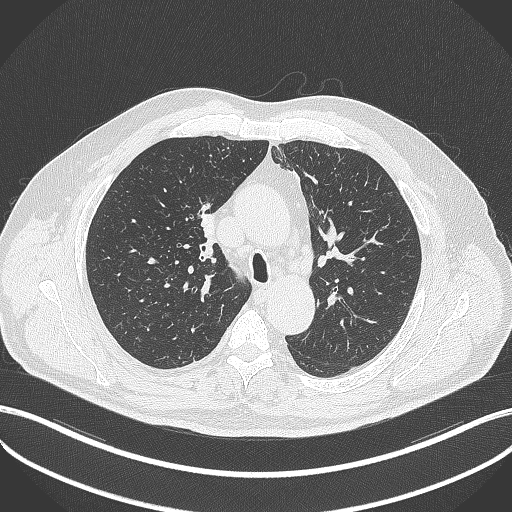
Chest CT, one axial slice. Slice 263 of 411 in the series (ordered by position). Reconstruction kernel B70f. Lung window (W 1500 / L -600 HU). 512 × 512 image matrix. Patient: male, 60 years. From the clinical record (not read from this slice): clinical TNM (as recorded): T1b N1 M0.
Structures marked on this image (rectangle marked by the reading radiologist):
- lung tumour (recorded histology: squamous cell carcinoma): bounding box (x1, y1, x2, y2) in pixels: (197, 208, 224, 250)